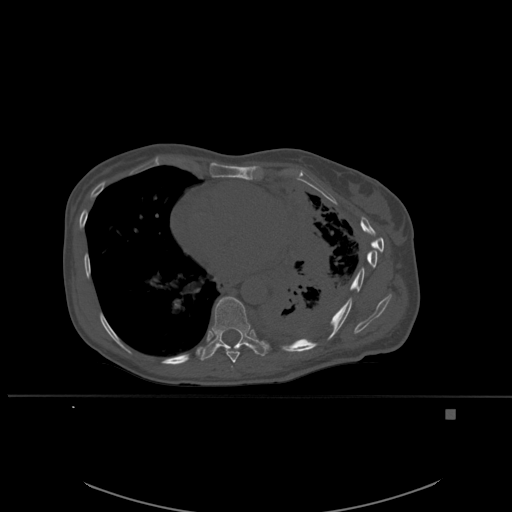
CT including the spine, one axial slice; slice 340 of 537 in the series (ordered by position); bone window (W 1800 / L 400 HU); 1.5 mm slice thickness; 512 × 512 image matrix. Patient: female, 45 years. Case-level facts recorded for this patient, not image findings: primary cancer: lung.
Outlined on this slice (semi-automatically segmented with operator editing):
- T8 vertebra: bounding box <217,346,240,363> (left, top, right, bottom; pixels)
- T9 vertebra: <200,296,269,361>